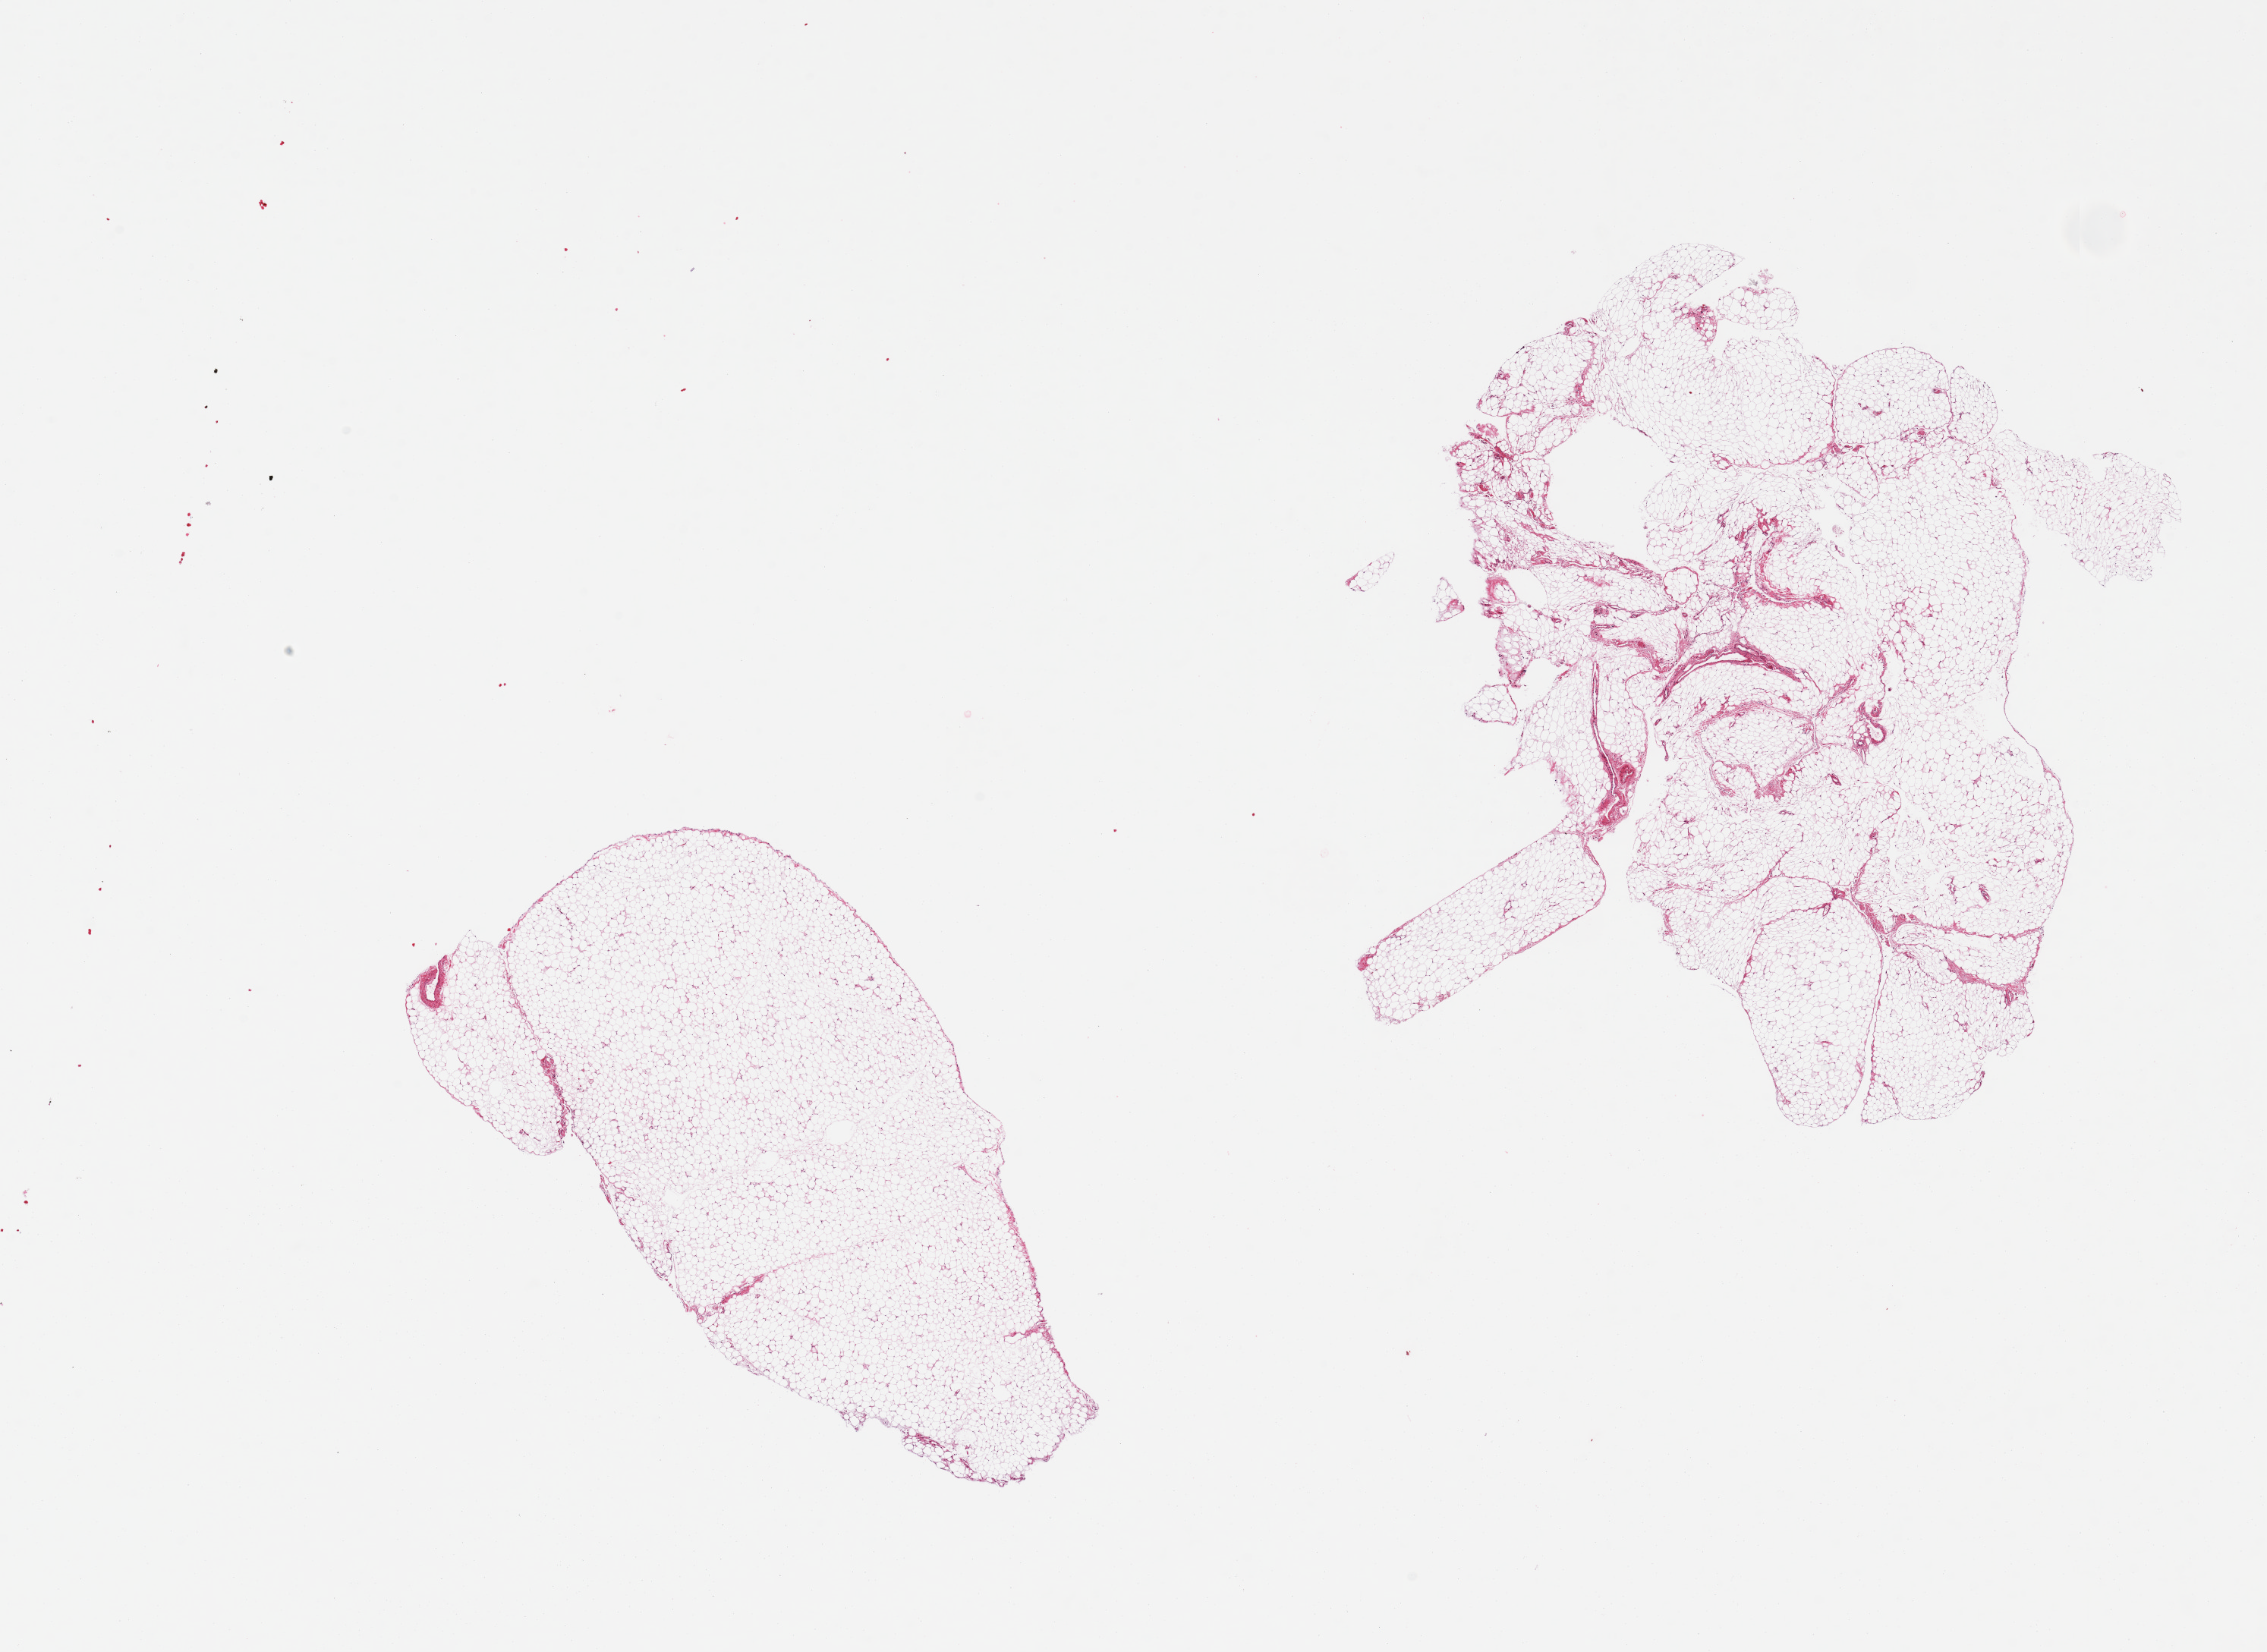
Whole-slide image, hematoxylin and eosin (H&E) stain, brightfield — low-resolution overview of the scanned area, about 23.6 x 17.2 mm (from a 20x scan); PAXgene-fixed paraffin-embedded (PFPE) section; sampled site (target tissue): omentum; donor tissue sample. Male donor.
Review note (as recorded): 2 pieces; fatty tissue with <5% stroma.